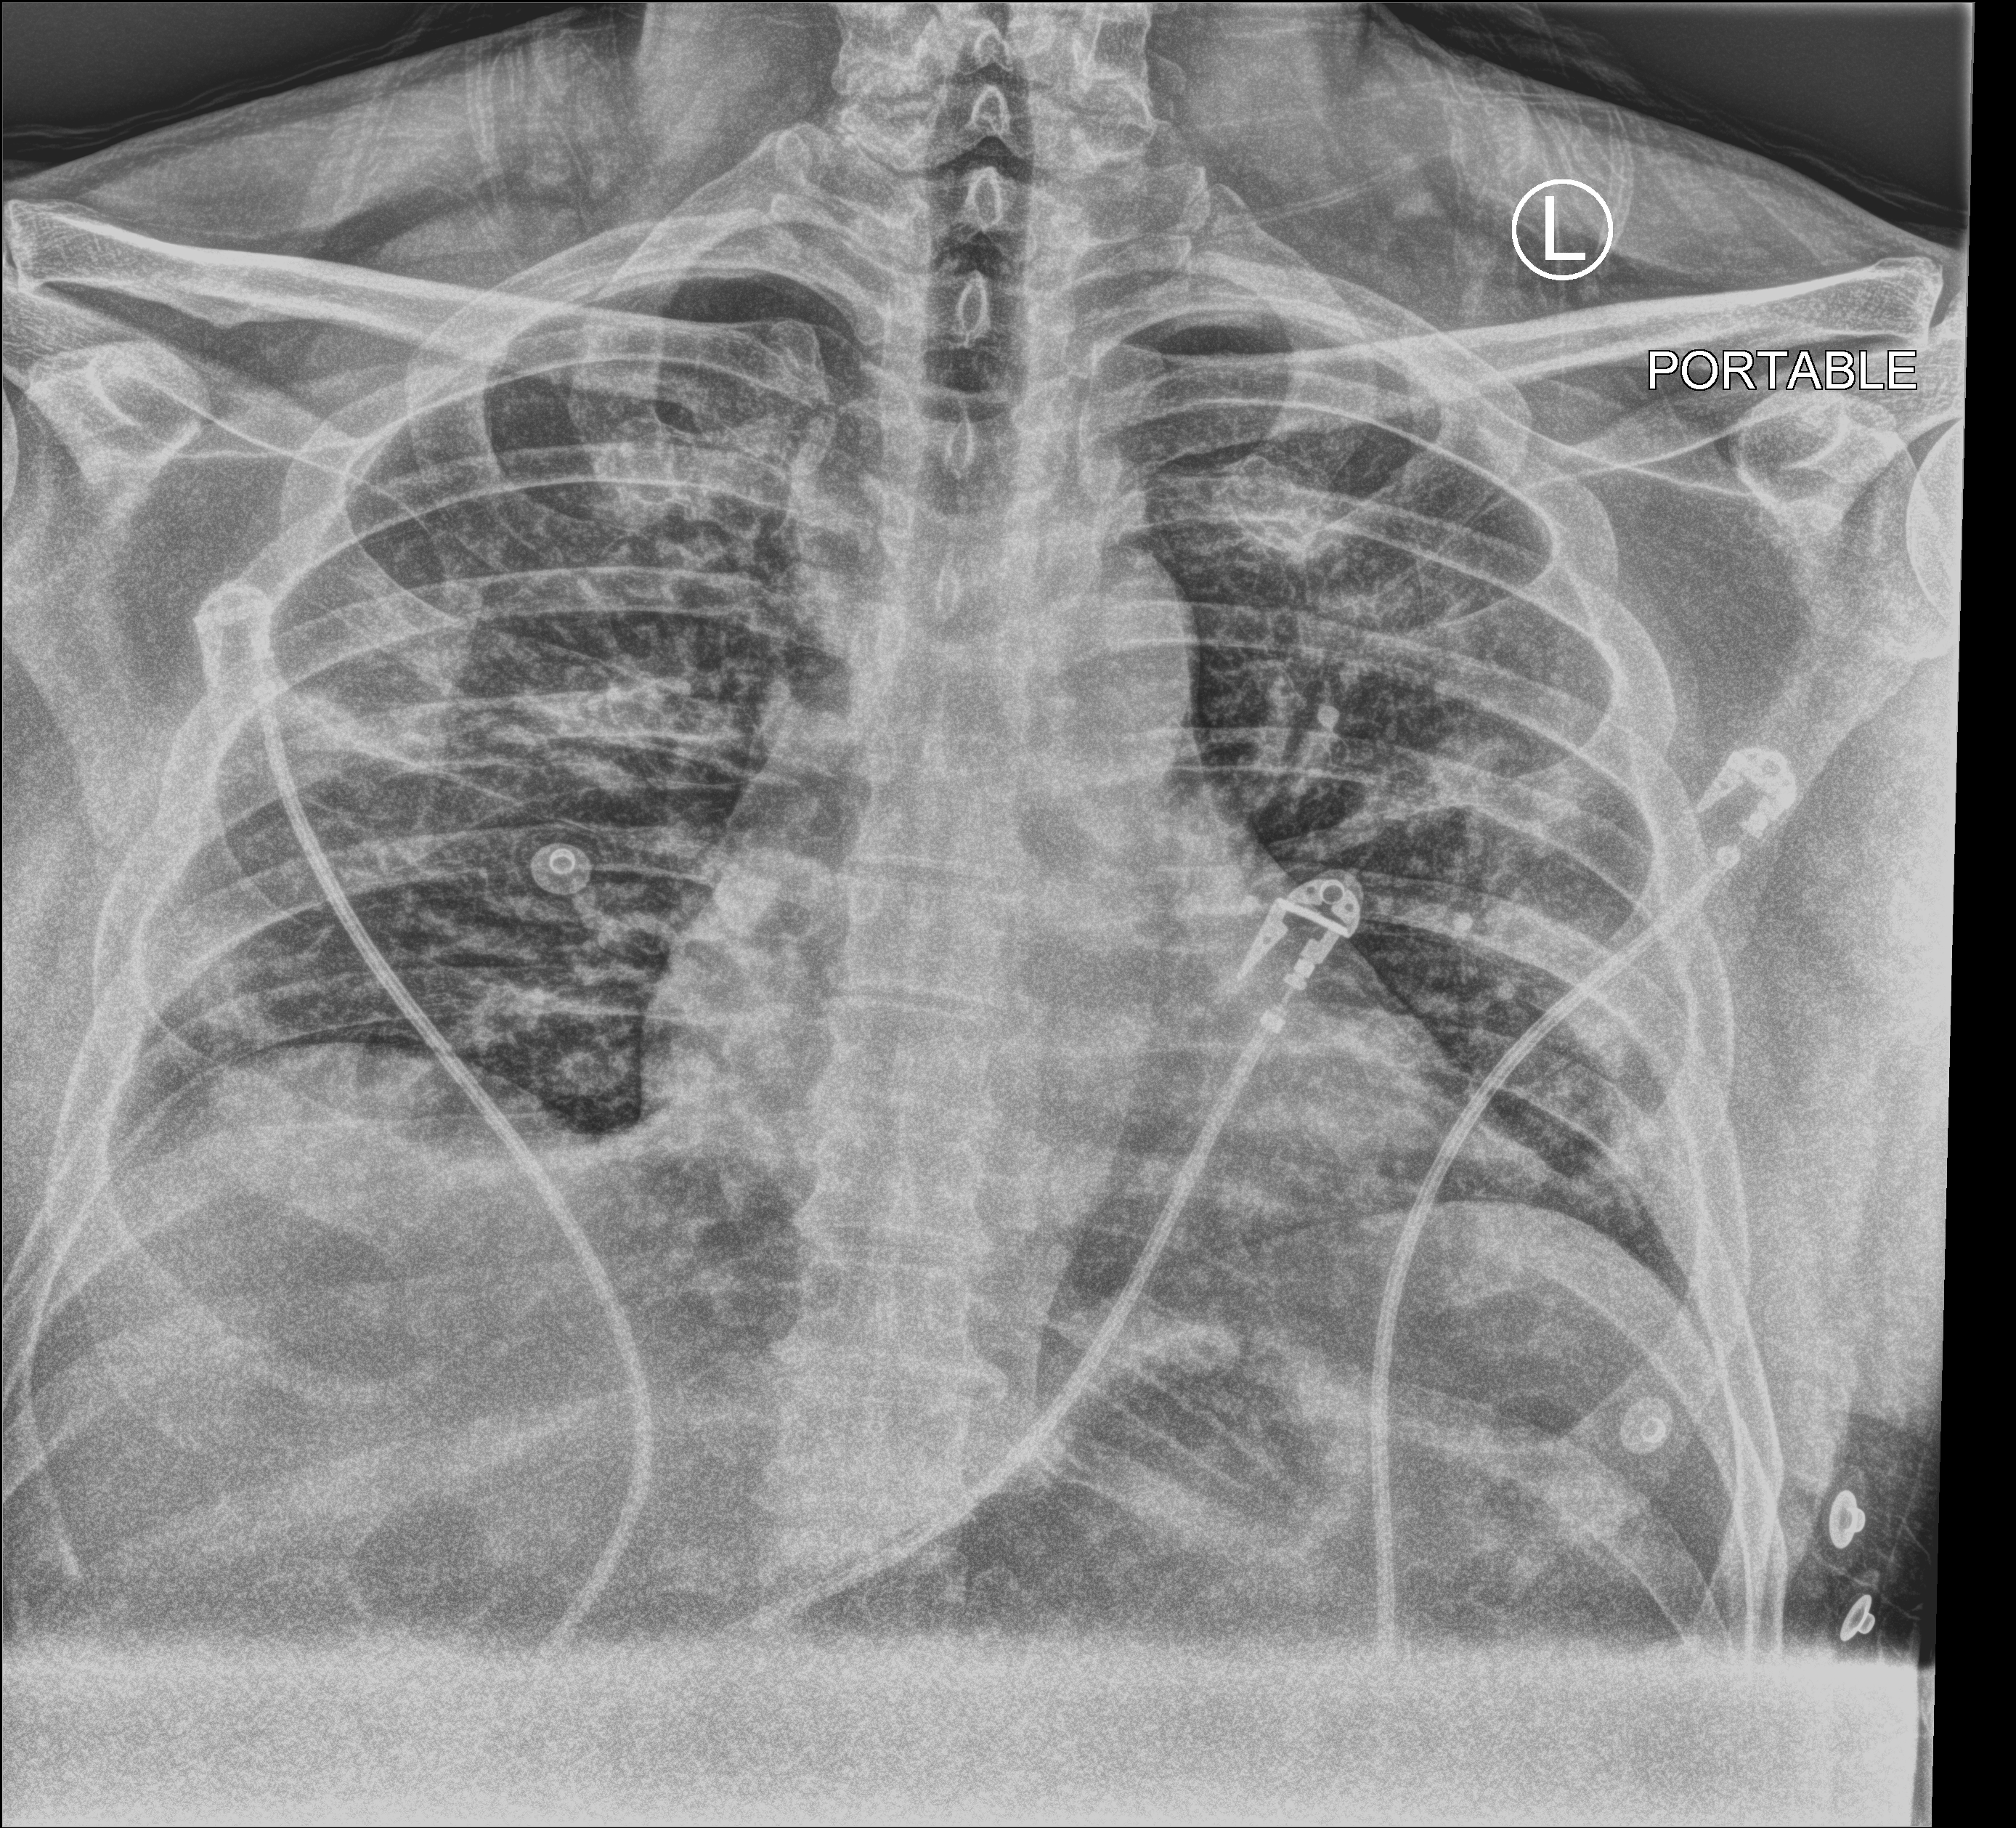
Chest X-ray (portable), anteroposterior (AP) projection. Patient hospitalised with COVID-19; male, aged 18–59 years.
From the hospital-stay record, not from the radiograph (when in the stay this image was taken is not recorded): mechanically ventilated during this hospital stay: no; smoking status (admission record): never.